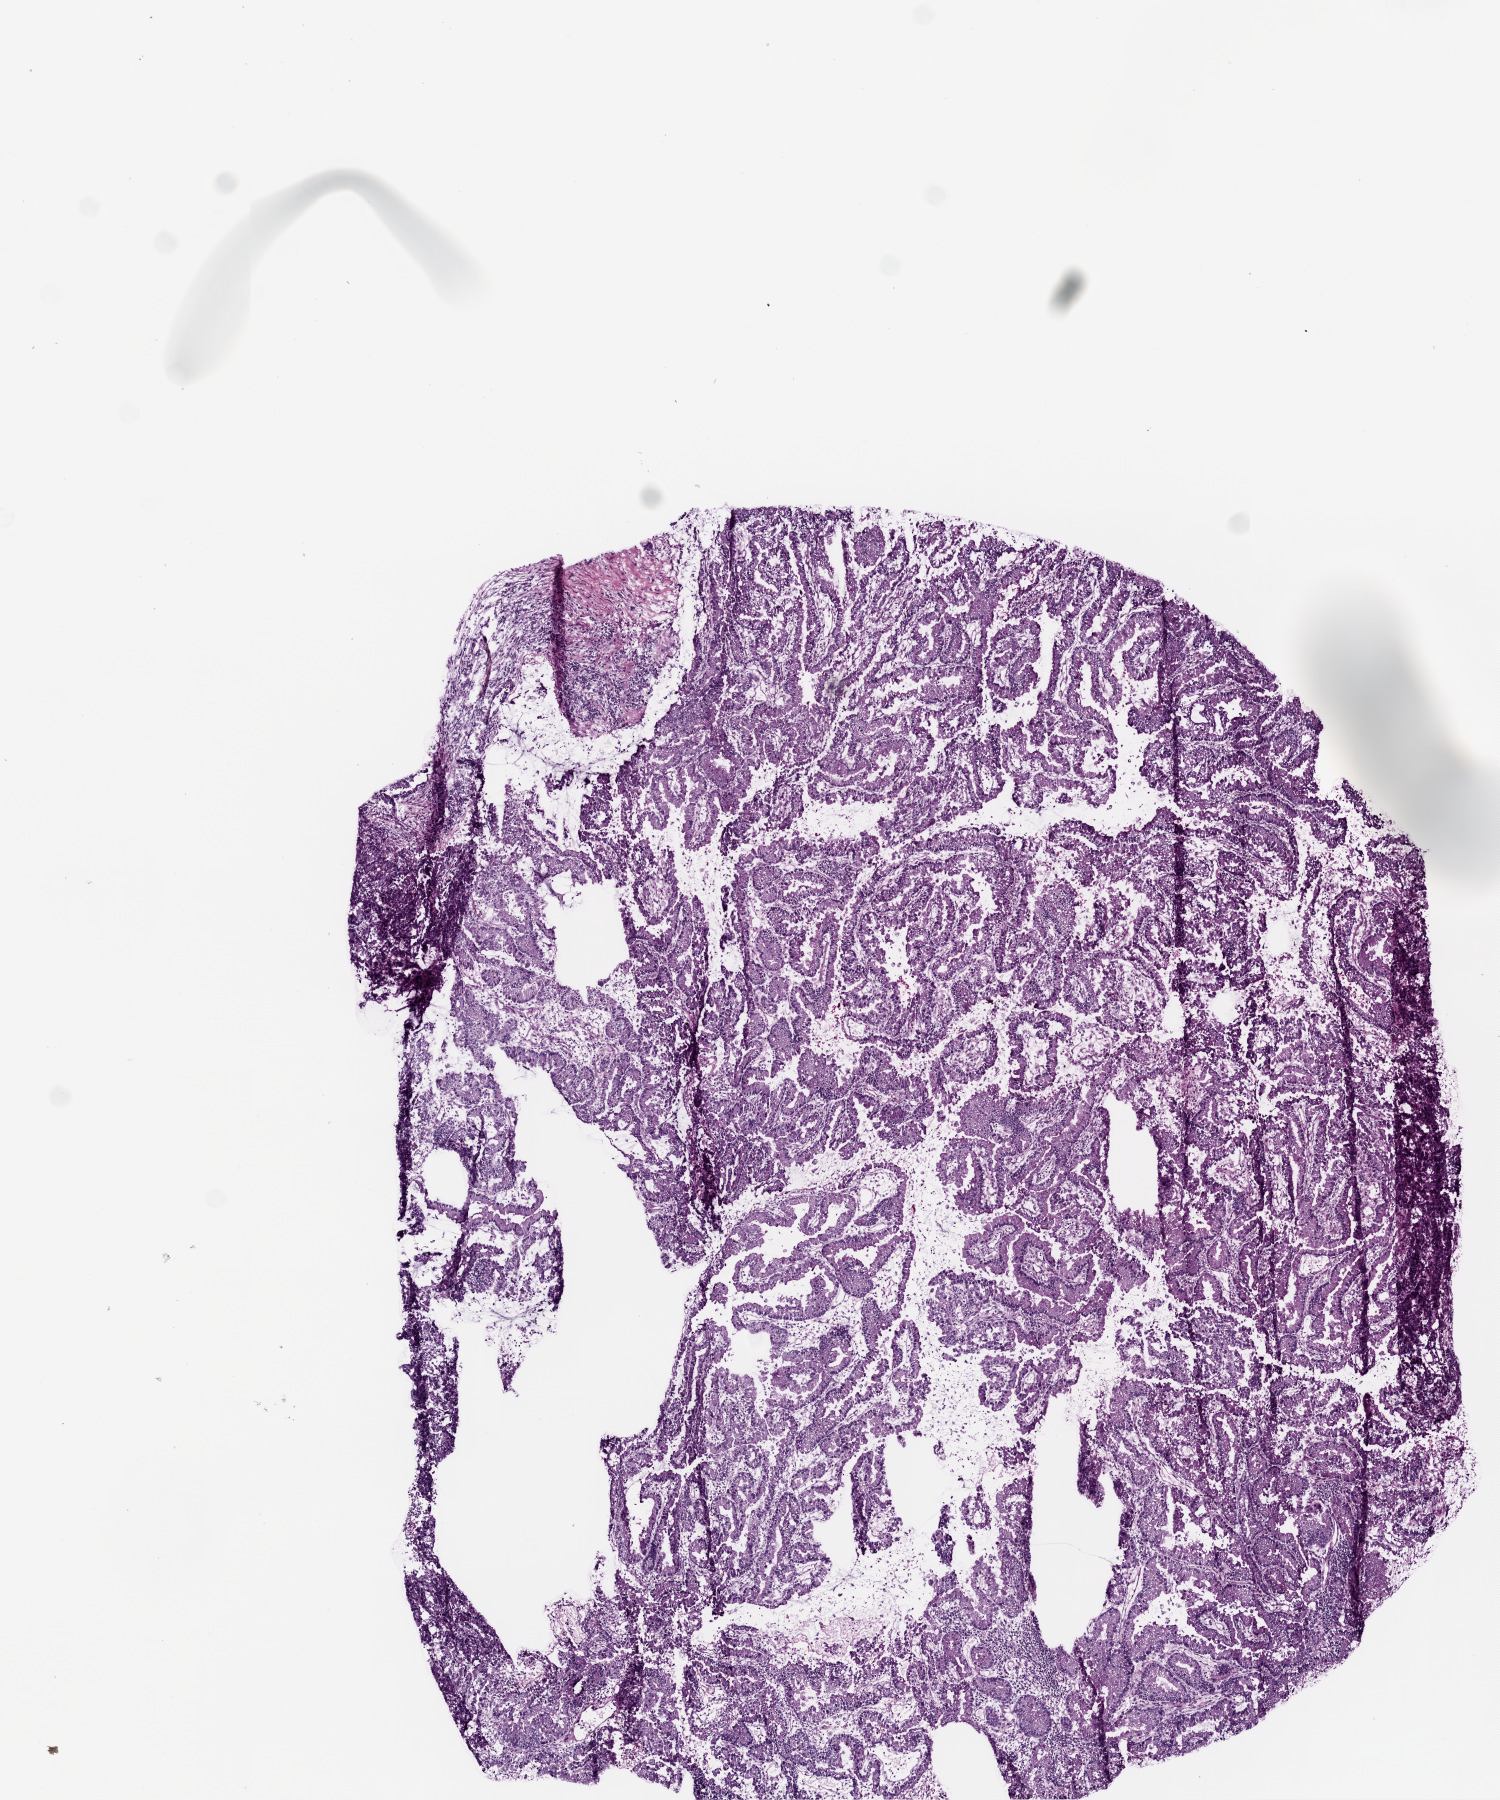
Whole-slide histology image, H&E, a low-resolution overview of the entire scanned area, about 6.0 x 7.2 mm (from a 20x scan), frozen section from the top of the tissue portion, primary tumour sample from the lung. Male patient; age at initial diagnosis 41 years. Composition of this section per pathologist review: tumour cells 85%, tumour nuclei 80%, normal cells 0%, stromal cells 15%, necrosis 0%.
• pathologic diagnosis: Adenocarcinoma with mixed subtypes
• AJCC pathologic stage: IB (6th edition)
• TNM: T2 N0 M0